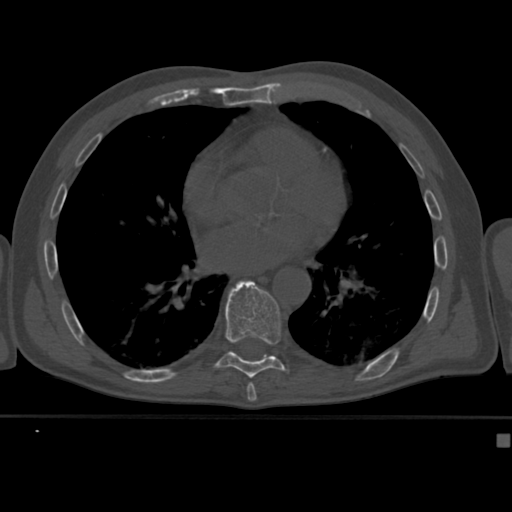
CT including the spine, one axial slice; slice 246 of 430 in the series (ordered by position); 120 kVp; bone window (W 1800 / L 400 HU); 1.5 mm slice thickness; 512 × 512 image matrix, field of view 337 × 337 mm. Patient: male, 64 years. From the clinical record (not read from this slice): primary cancer: uterus; vertebrae with lytic lesions (as recorded): T1, T4, T5, T7, L5.
Annotated regions visible in this slice (semi-automatic segmentation, software-assisted and operator-edited):
- T9 vertebra: bounding box (x1, y1, x2, y2) in pixels: (214, 280, 290, 378)